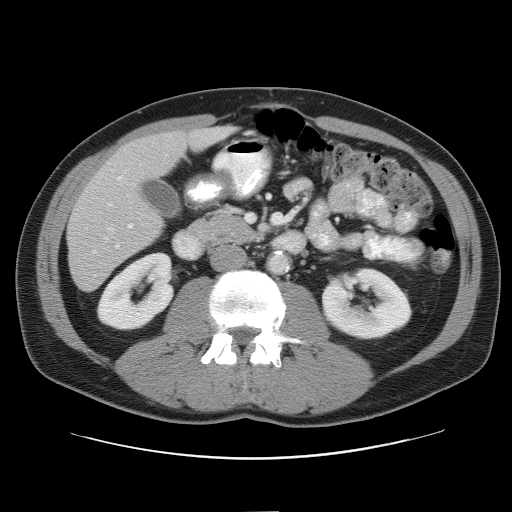
Contrast-enhanced abdominal CT, one axial slice; slice 23 of 52 in the series (ordered by position); intravenous contrast given; soft-tissue window (W 400 / L 40 HU); 5 mm slice thickness; 512 × 512 image matrix, field of view 393 × 393 mm. Male patient, age 70 years. Case-level facts recorded for this patient, not image findings: diagnosis: colorectal cancer liver metastases, imaged before liver resection; multiple liver metastases: yes.
Outlined on this slice (outlined manually by an expert reader):
- hepatic veins: bounding box <77,208,120,254> (left, top, right, bottom; pixels)
- liver: <68,128,228,290>
- planned liver remnant (the part of the liver to remain after resection): <119,128,228,180>
- portal vein (with intrahepatic branches): <108,176,133,229>